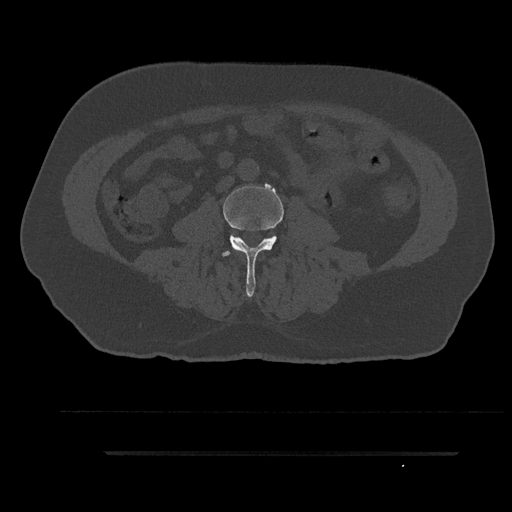
CT including the spine, one axial slice; slice 32 of 797 in the series (ordered by position); bone window (W 1800 / L 400 HU); 512 × 512 image matrix, field of view 432 × 432 mm. Male patient, age 63 years. From the clinical record (not read from this slice): primary cancer: renal.
Annotated regions visible in this slice (semi-automatically segmented with operator editing):
- L3 vertebra: bounding box [x1, y1, x2, y2] px = [222, 185, 284, 297]